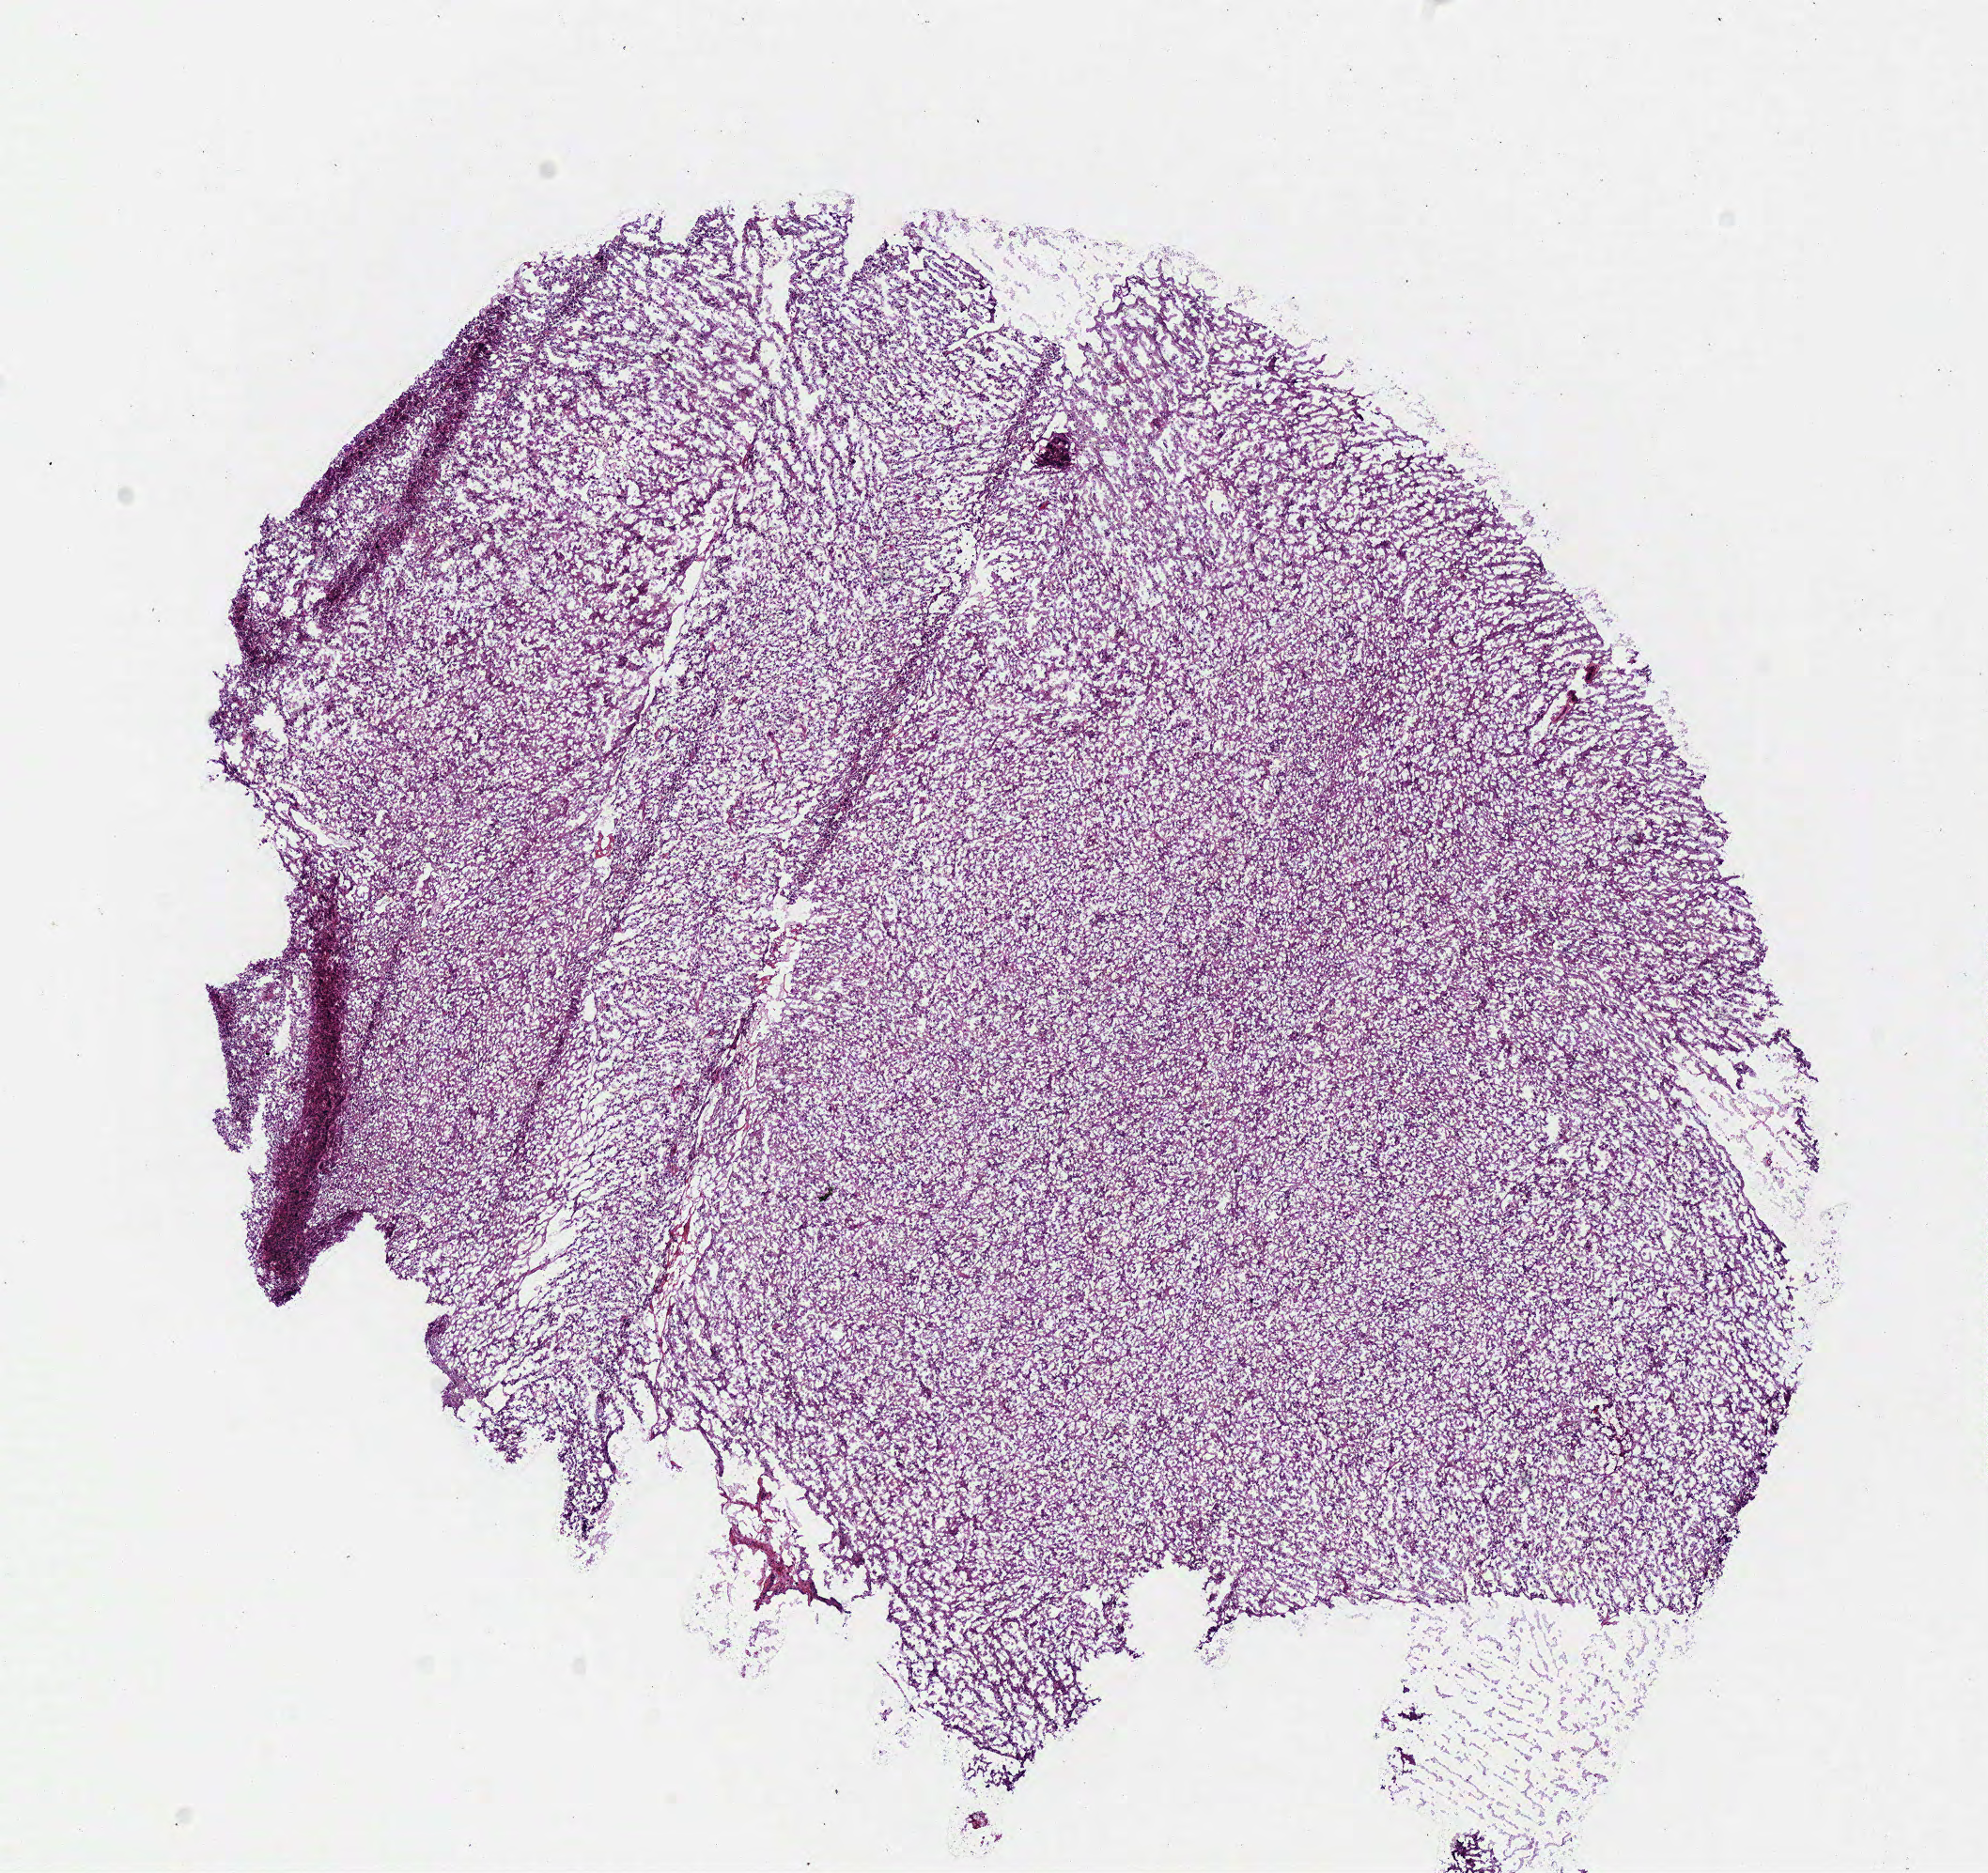
Digitized Hematoxylin and eosin (H&E) stained tissue section (whole slide) — a low-resolution overview of the entire scanned area, about 8.3 x 7.8 mm (acquisition: 40x scan), frozen section from the bottom of the tissue portion, sample: primary tumour, brain. Male, age 52 years at initial diagnosis. Histologic grade: G3 (poorly differentiated). Pathologist review of this section (percent, as recorded): tumour cells 100%, tumour nuclei 85%, normal cells 0%, stromal cells 0%, necrosis 0%.
Pathologic diagnosis: Astrocytoma, anaplastic (cerebrum).